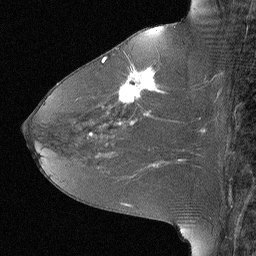
Breast MRI (dynamic contrast-enhanced), one sagittal slice; position 33 of 64 along the scan axis; dynamic contrast-enhanced study with each time point stored as its own series, time point 2 of 3 at this slice position (early post-contrast, ordered by acquisition time); 1.5 T; TE 4 ms, TR 30 ms; 2.25 mm slice thickness; 256 × 256 image matrix, field of view 180 × 180 mm. Patient: female, 46 years. Case-level facts recorded for this patient, not image findings: setting: breast cancer imaged before/during neoadjuvant chemotherapy; receptor status: HR-positive, HER2-negative.
Annotated regions visible in this slice (semi-automatic segmentation, software-assisted and operator-edited):
- analysis volume of interest (the breast-tissue region the enhancement analysis was run in; not a lesion): bounding box <106,43,184,119> (left, top, right, bottom; pixels)
- tumour enhancement mask (voxels above the 90 % enhancement threshold inside the analysis volume of interest): <119,66,159,103>